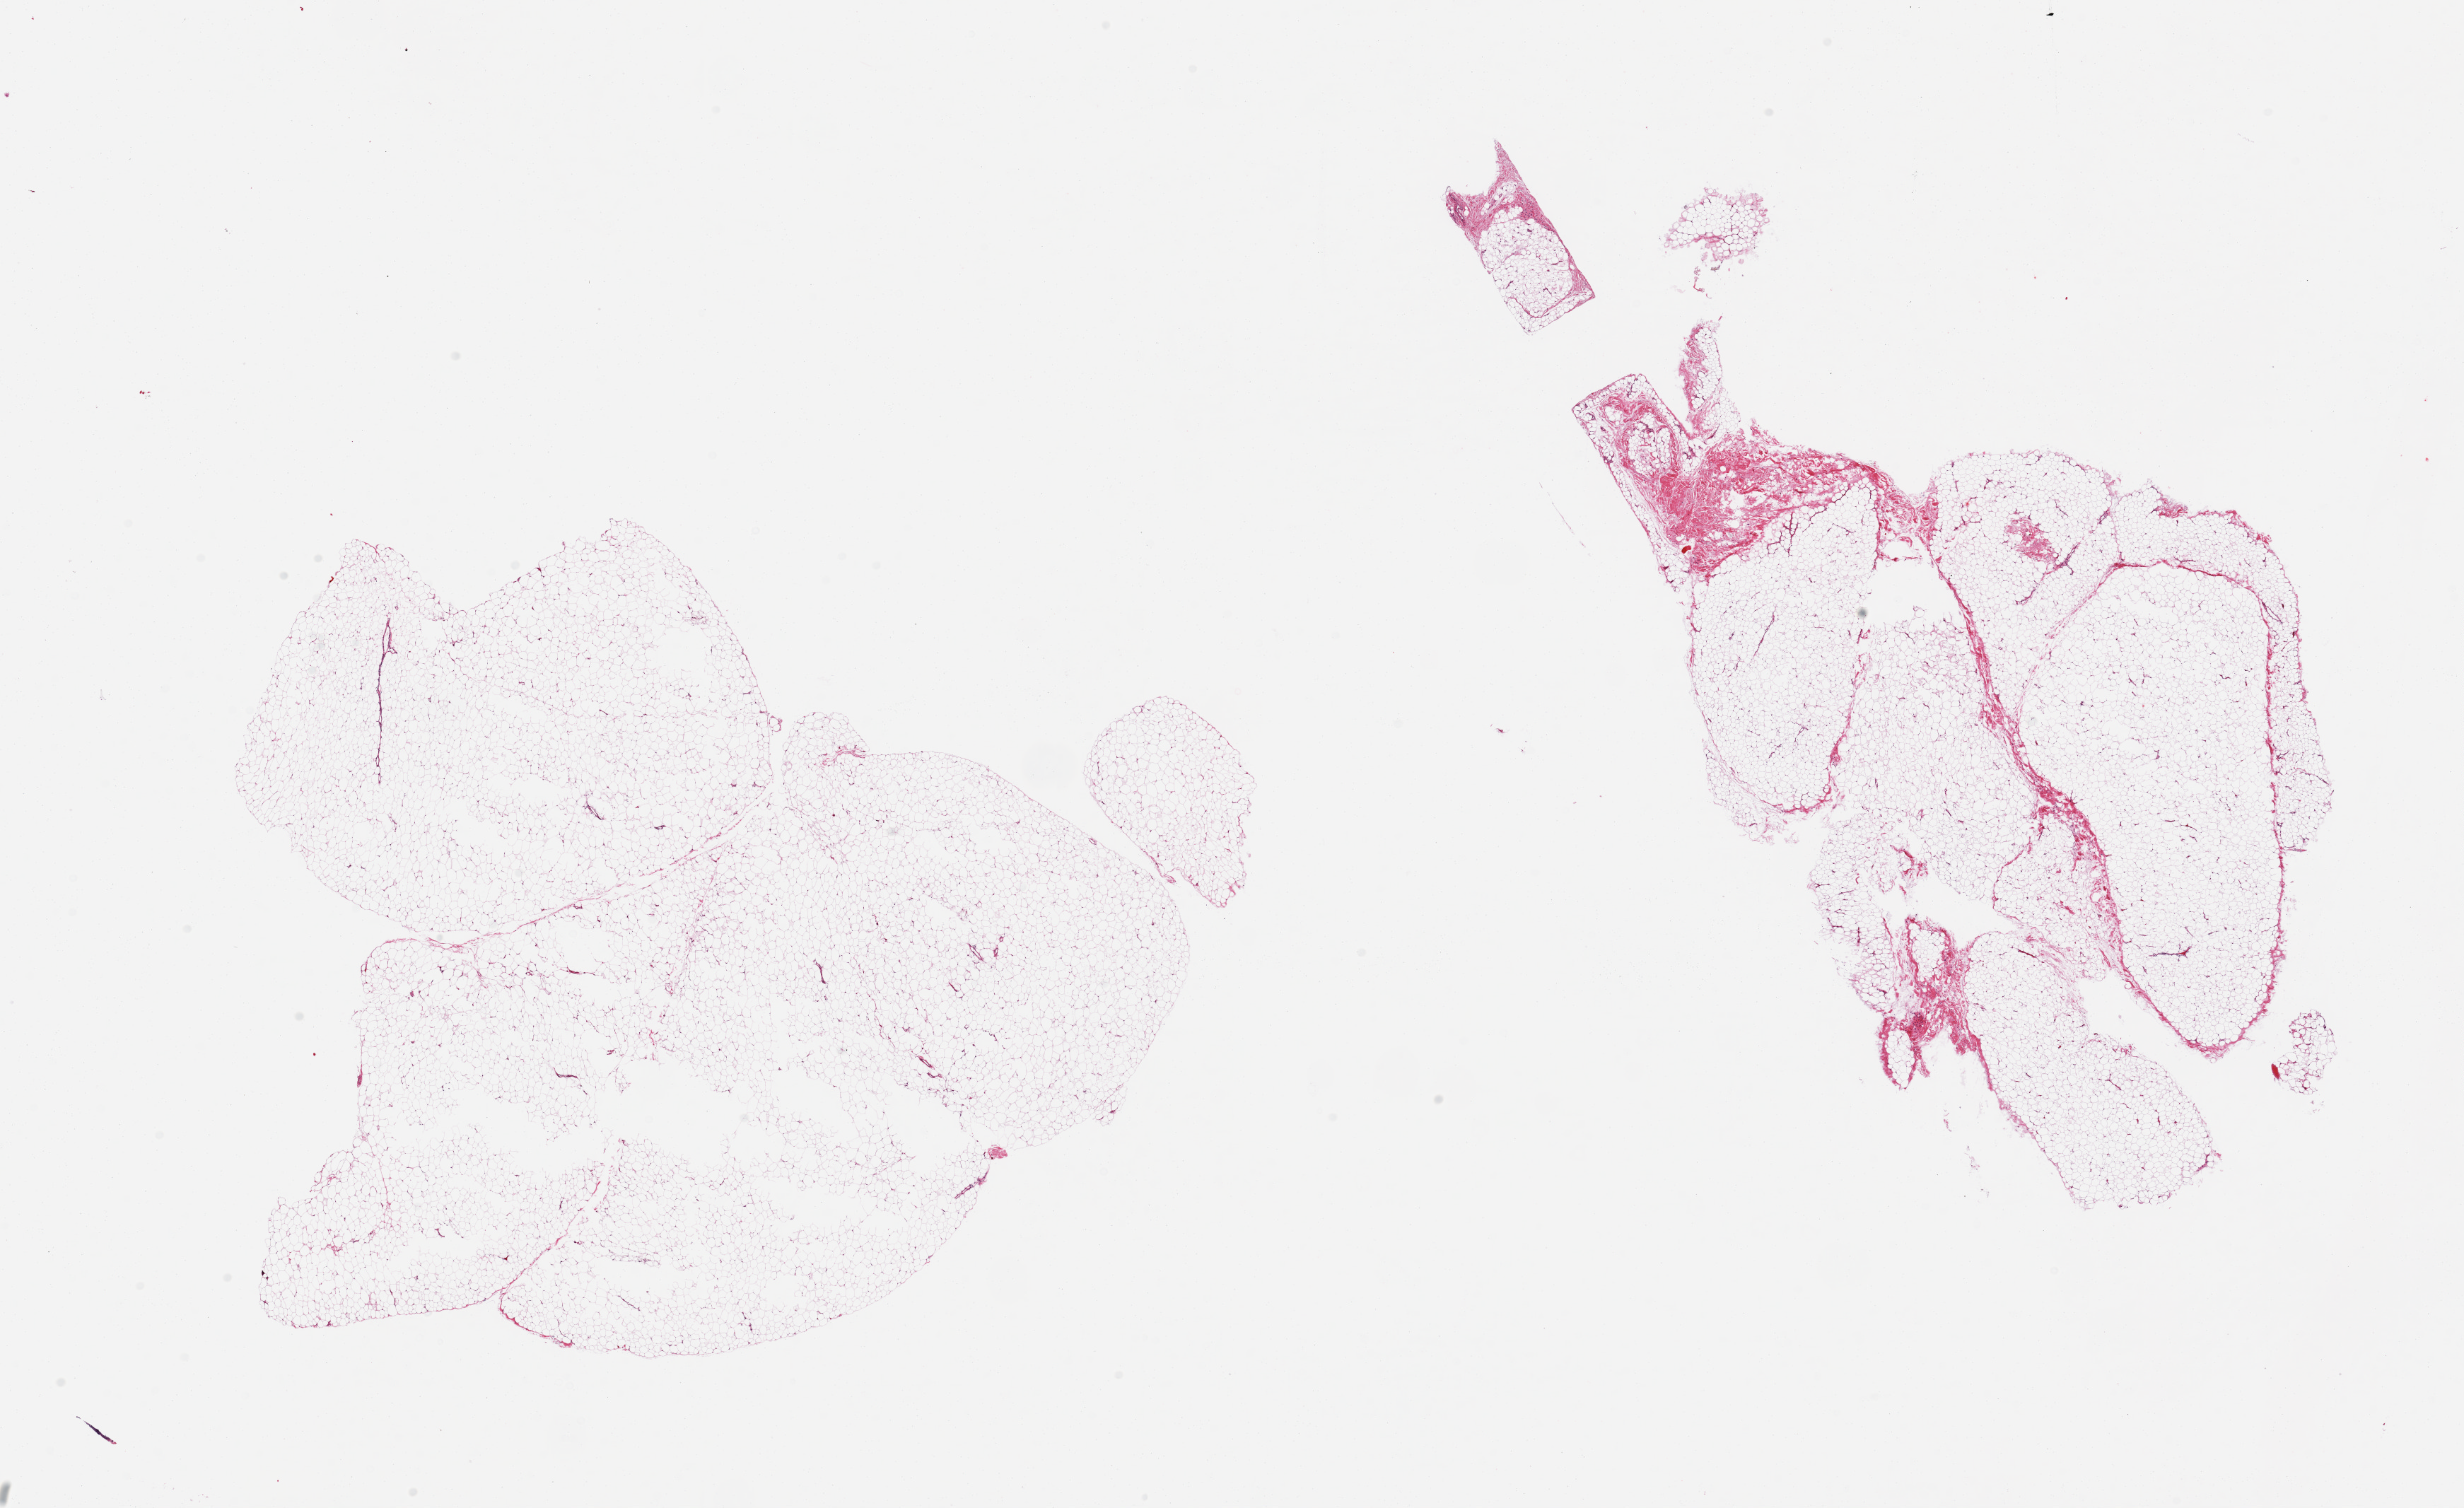
Digitized haematoxylin and eosin-stained section, a low-resolution overview of the entire scanned area, about 27.6 x 16.9 mm (slide scanned at 20x), PAXgene-fixed, paraffin-embedded tissue, target tissue: adipose tissue, tissue donor sample.
Review note (as recorded): 2 pieces, interstitial fascia is ~10%.